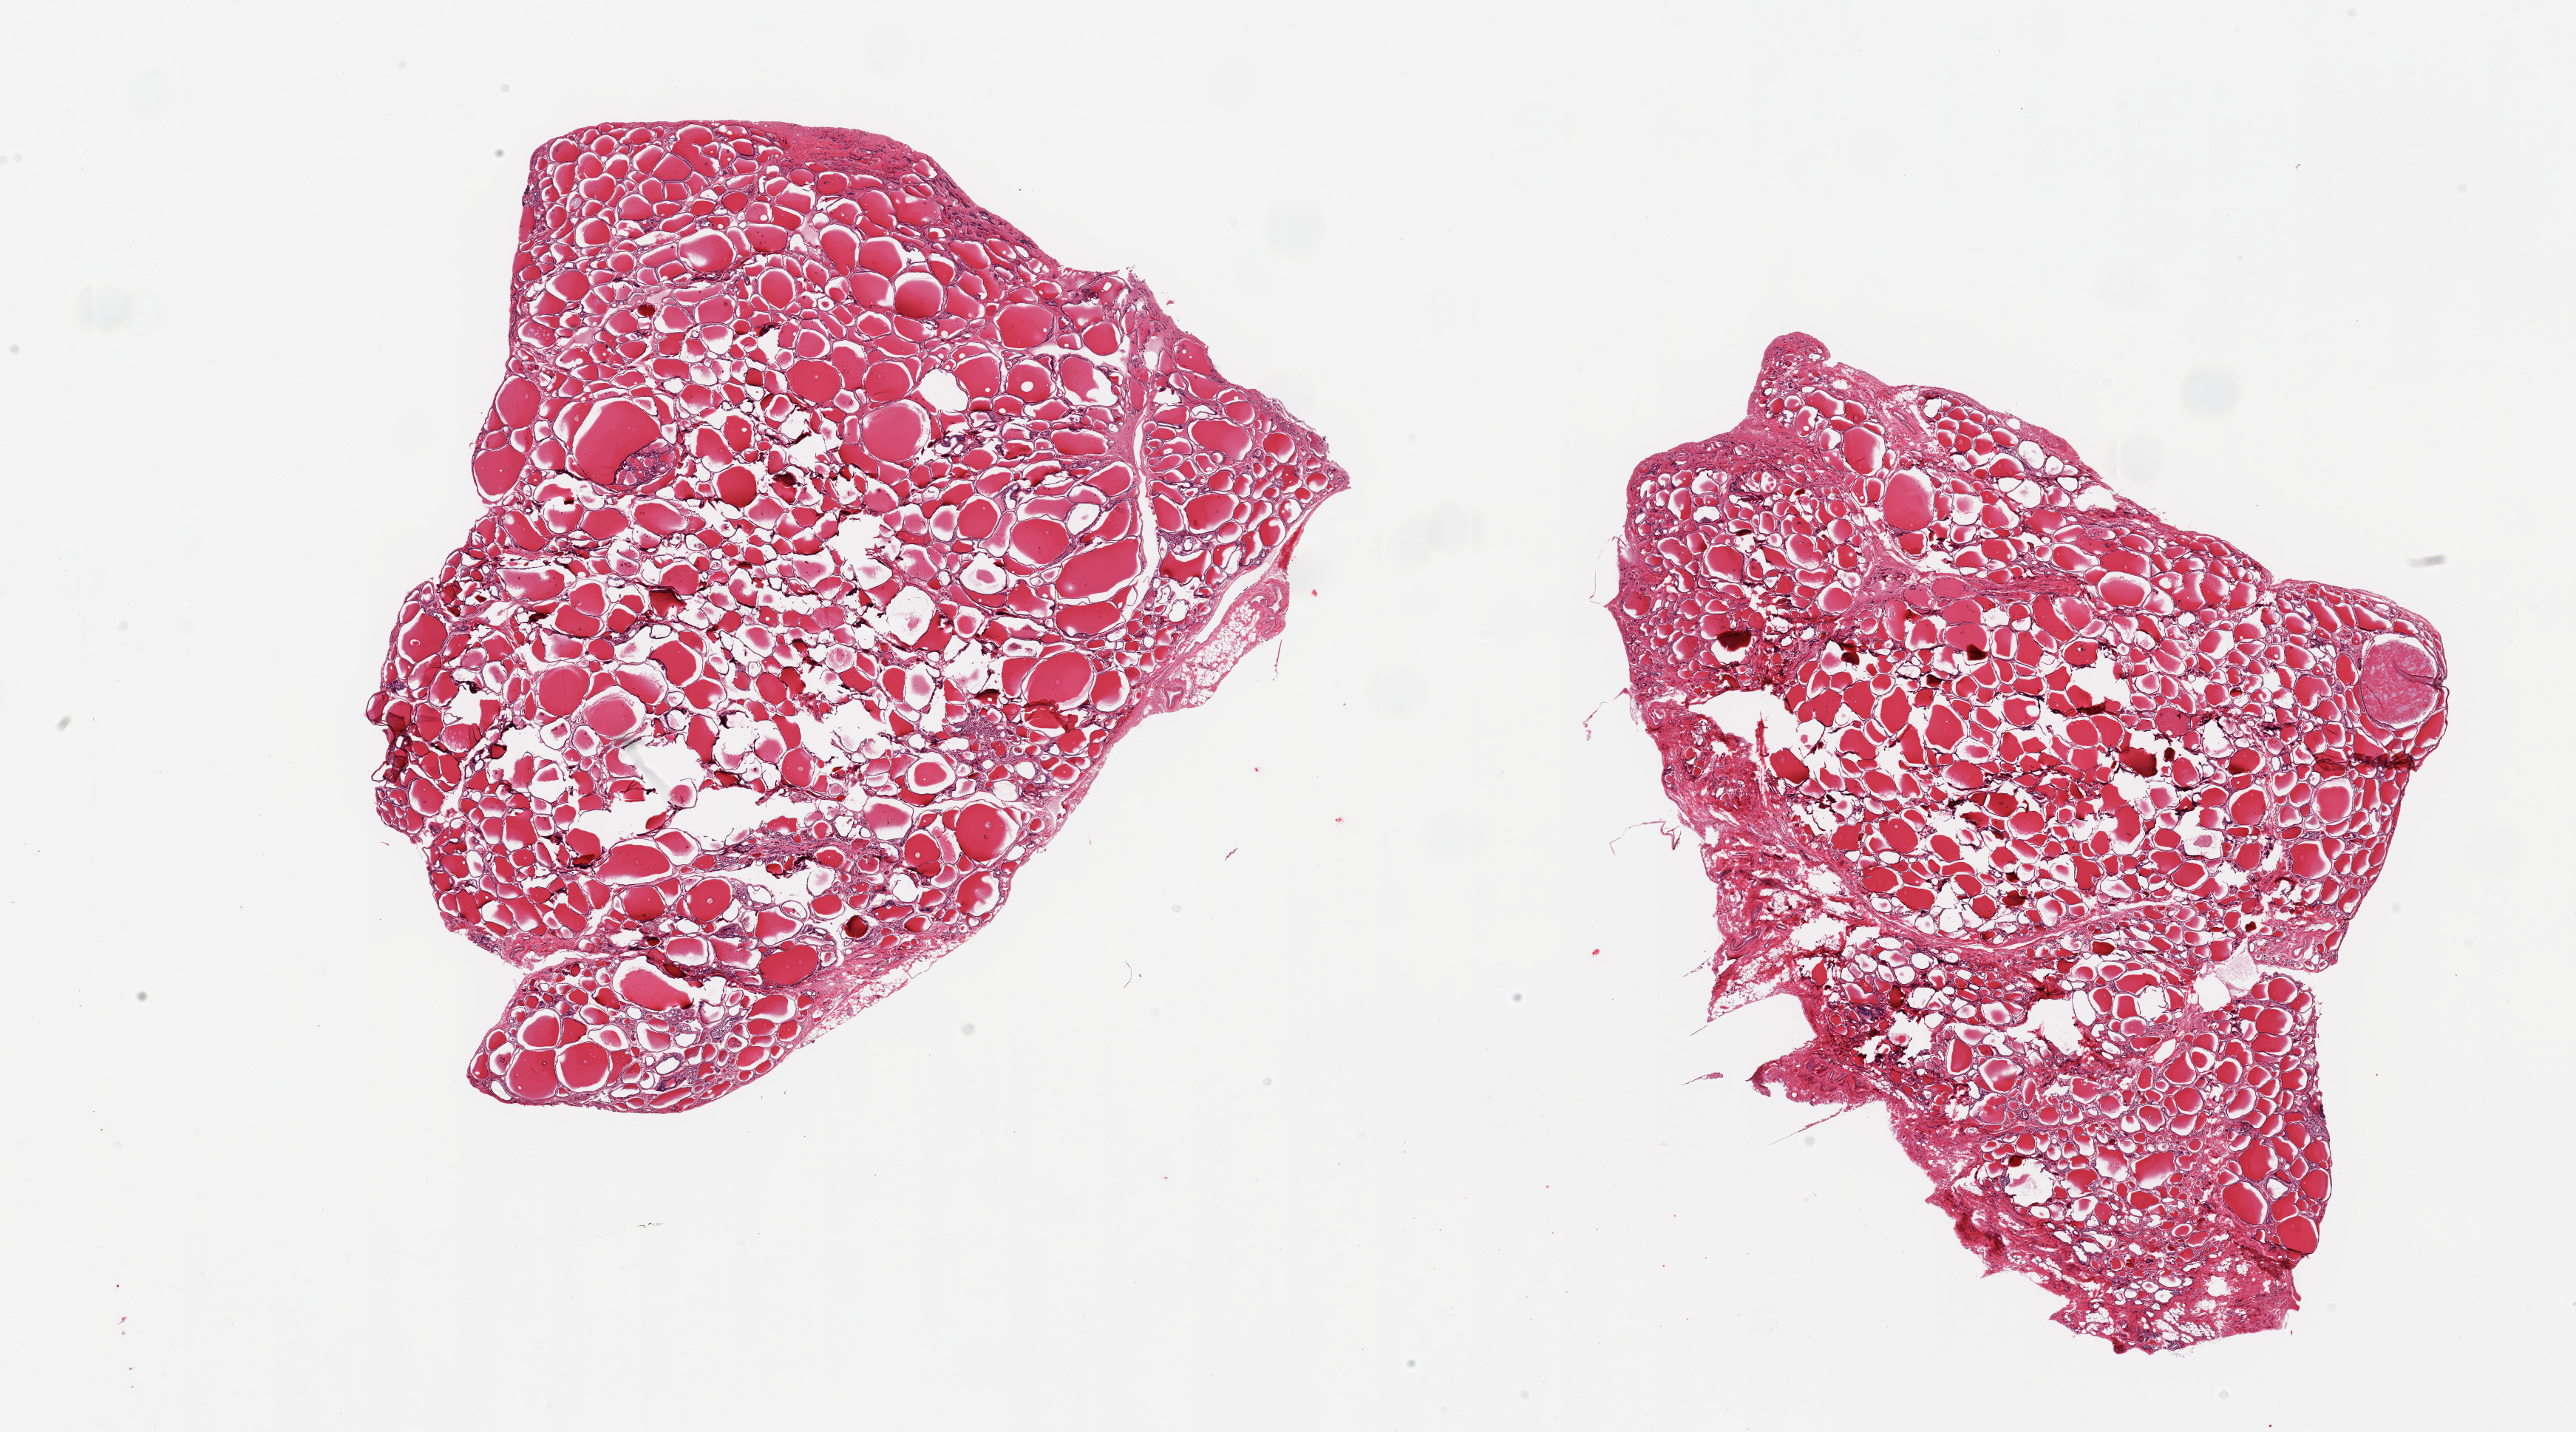
Haematoxylin and eosin whole-slide image — shown as a low-resolution overview of the whole scanned area (about 27.6 x 15.3 mm). PAXgene-fixed paraffin-embedded (PFPE) section. Sampled site (target tissue): thyroid. Tissue donor sample.
• review note (as recorded): 2 pieces